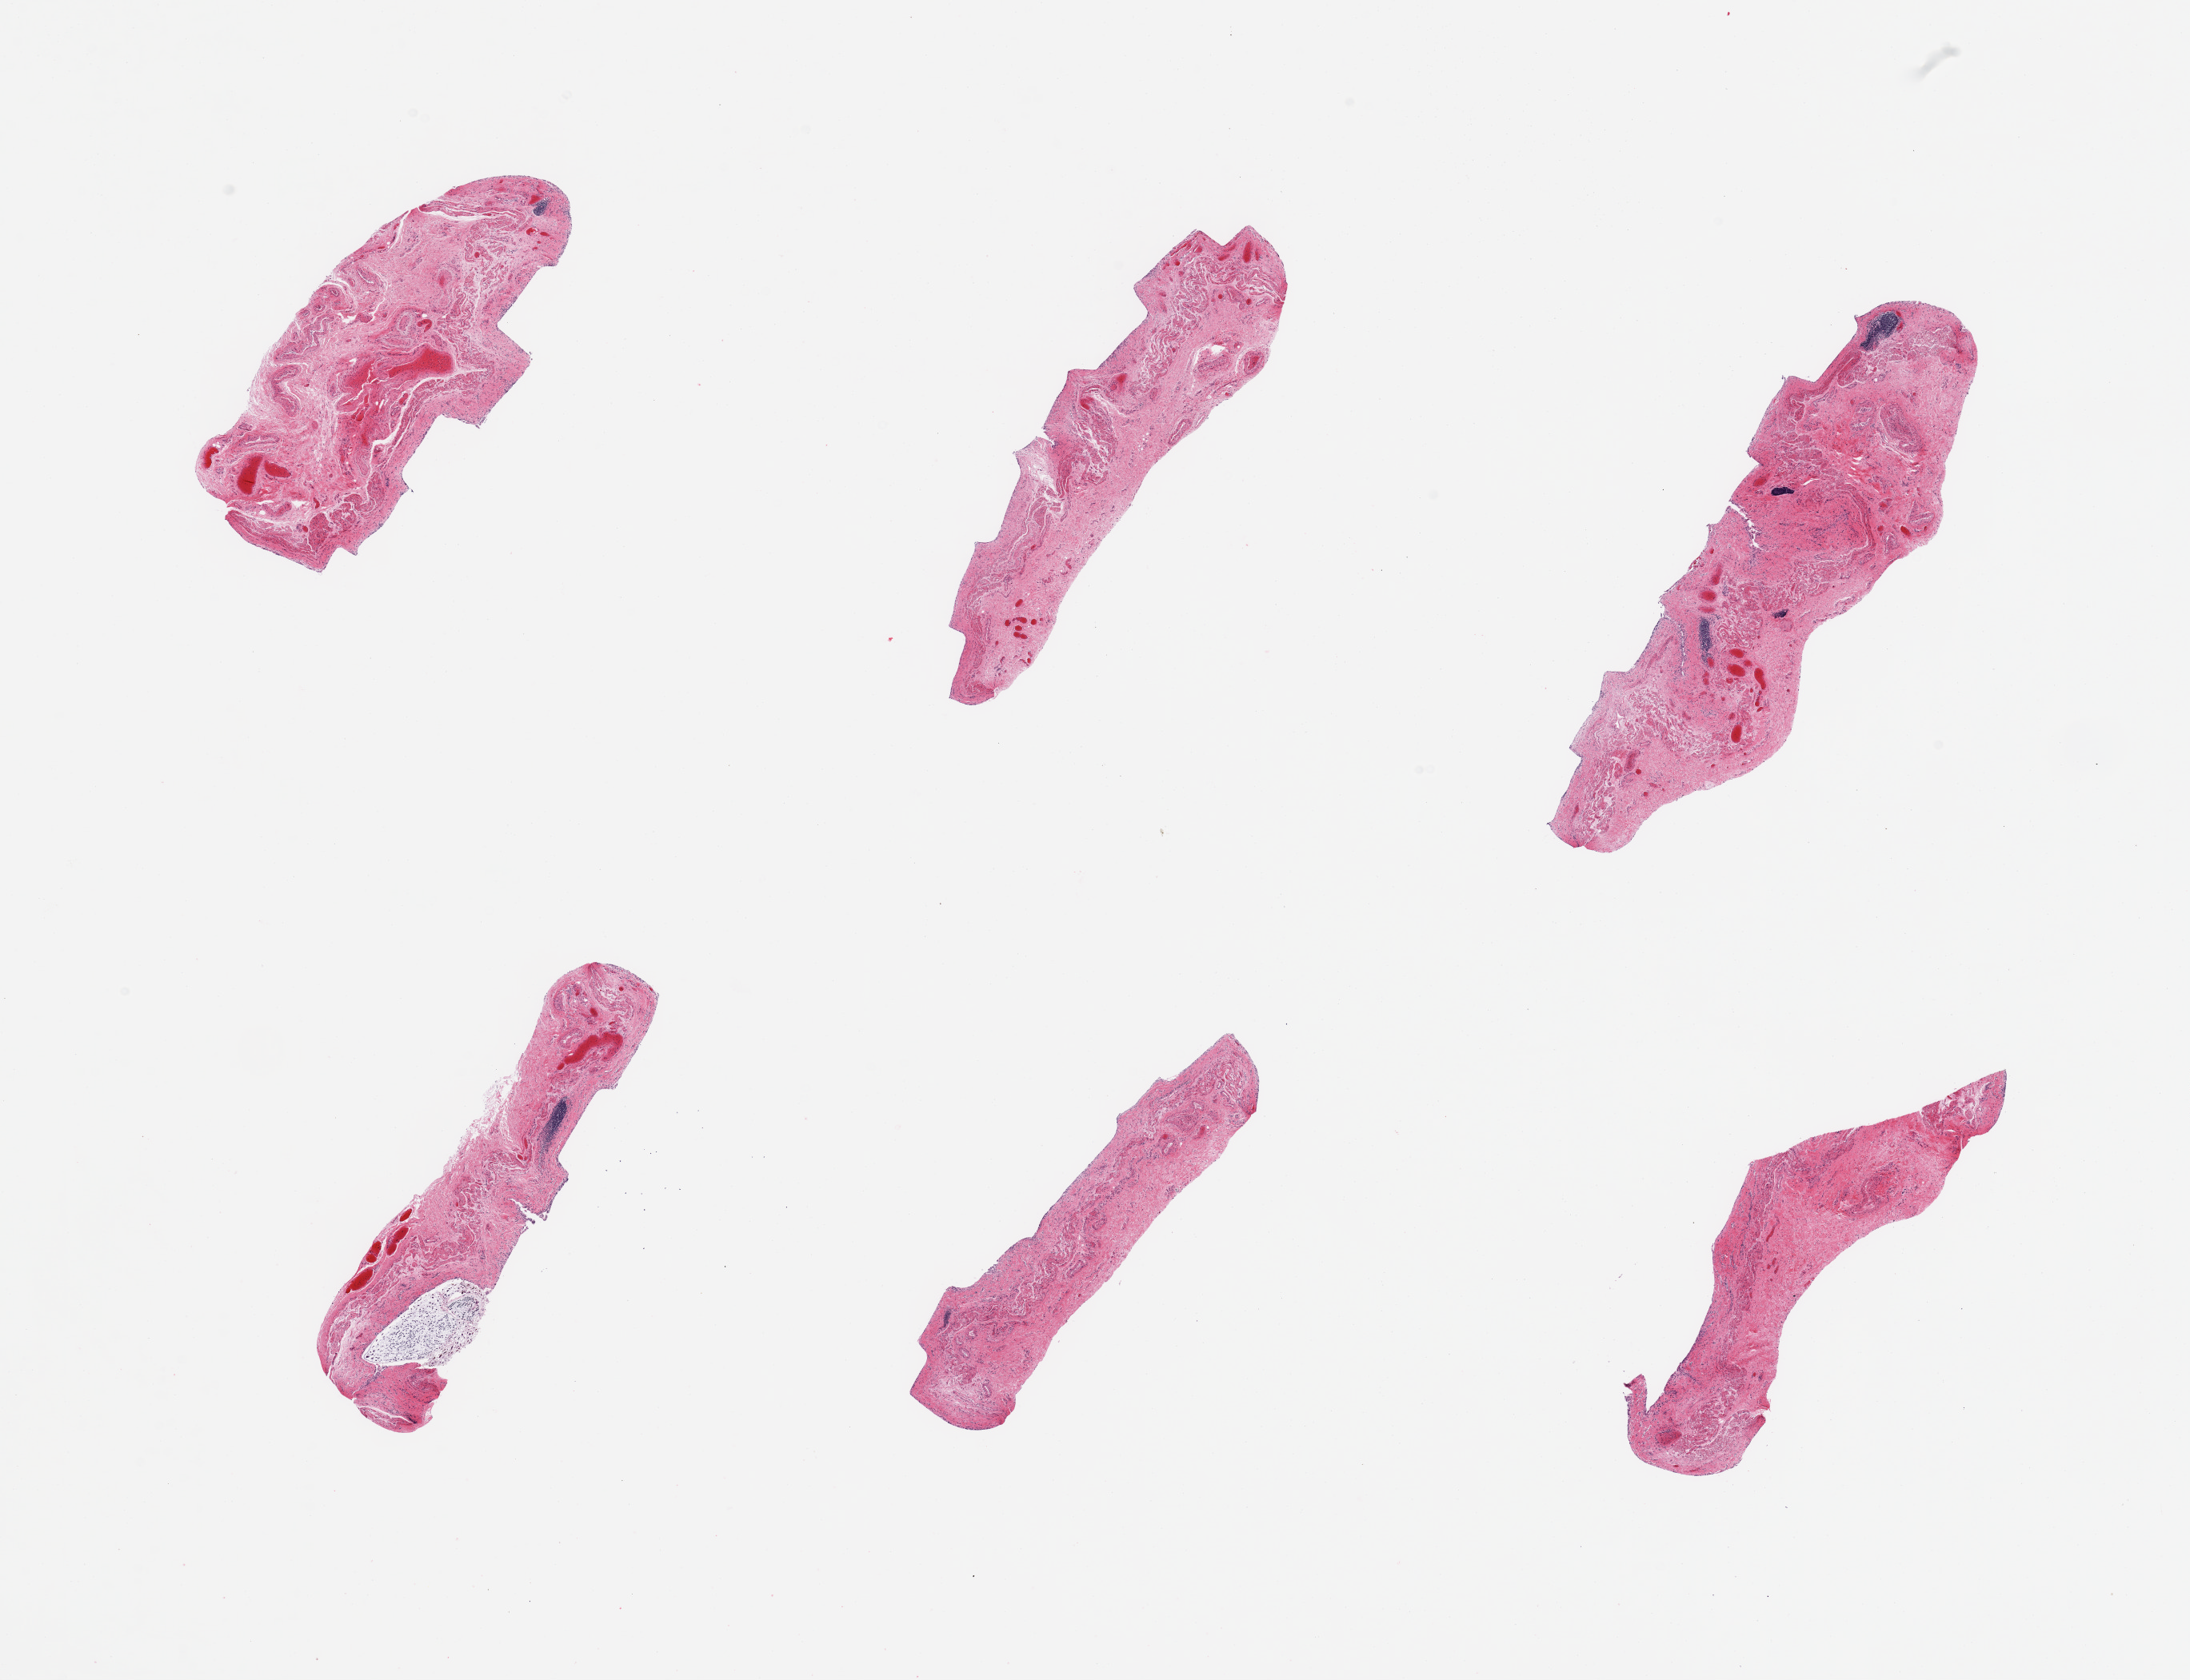
Whole-slide image, H&E stain, low-resolution overview of the scanned area, about 21.7 x 16.6 mm (slide scanned at 20x). PAXgene-fixed, paraffin-embedded tissue. Target tissue: esophageal mucous membrane. Donor tissue sample. Donor sex: male.
Review note (as recorded): 6 pieces; epithelium totally sloughed.